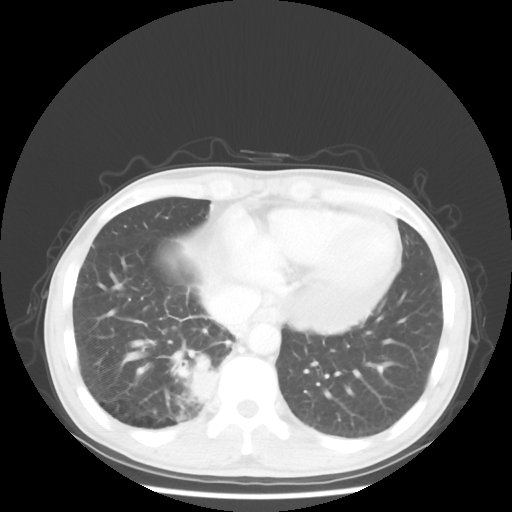
Chest CT, one axial slice; slice 13 of 58 in the series (ordered by position); 100 kVp; lung window (W 1500 / L -600 HU); 5 mm slice thickness; 512 × 512 image matrix, field of view 360 × 360 mm. Patient: male, 56 years. Case-level facts recorded for this patient, not image findings: clinical TNM (as recorded): T2 N1 M1; histopathological grade: G1.
Outlined on this slice (bounding box drawn by a radiologist):
- lung tumour (recorded histology: adenocarcinoma): box from (x=188, y=351) to (x=219, y=406) px